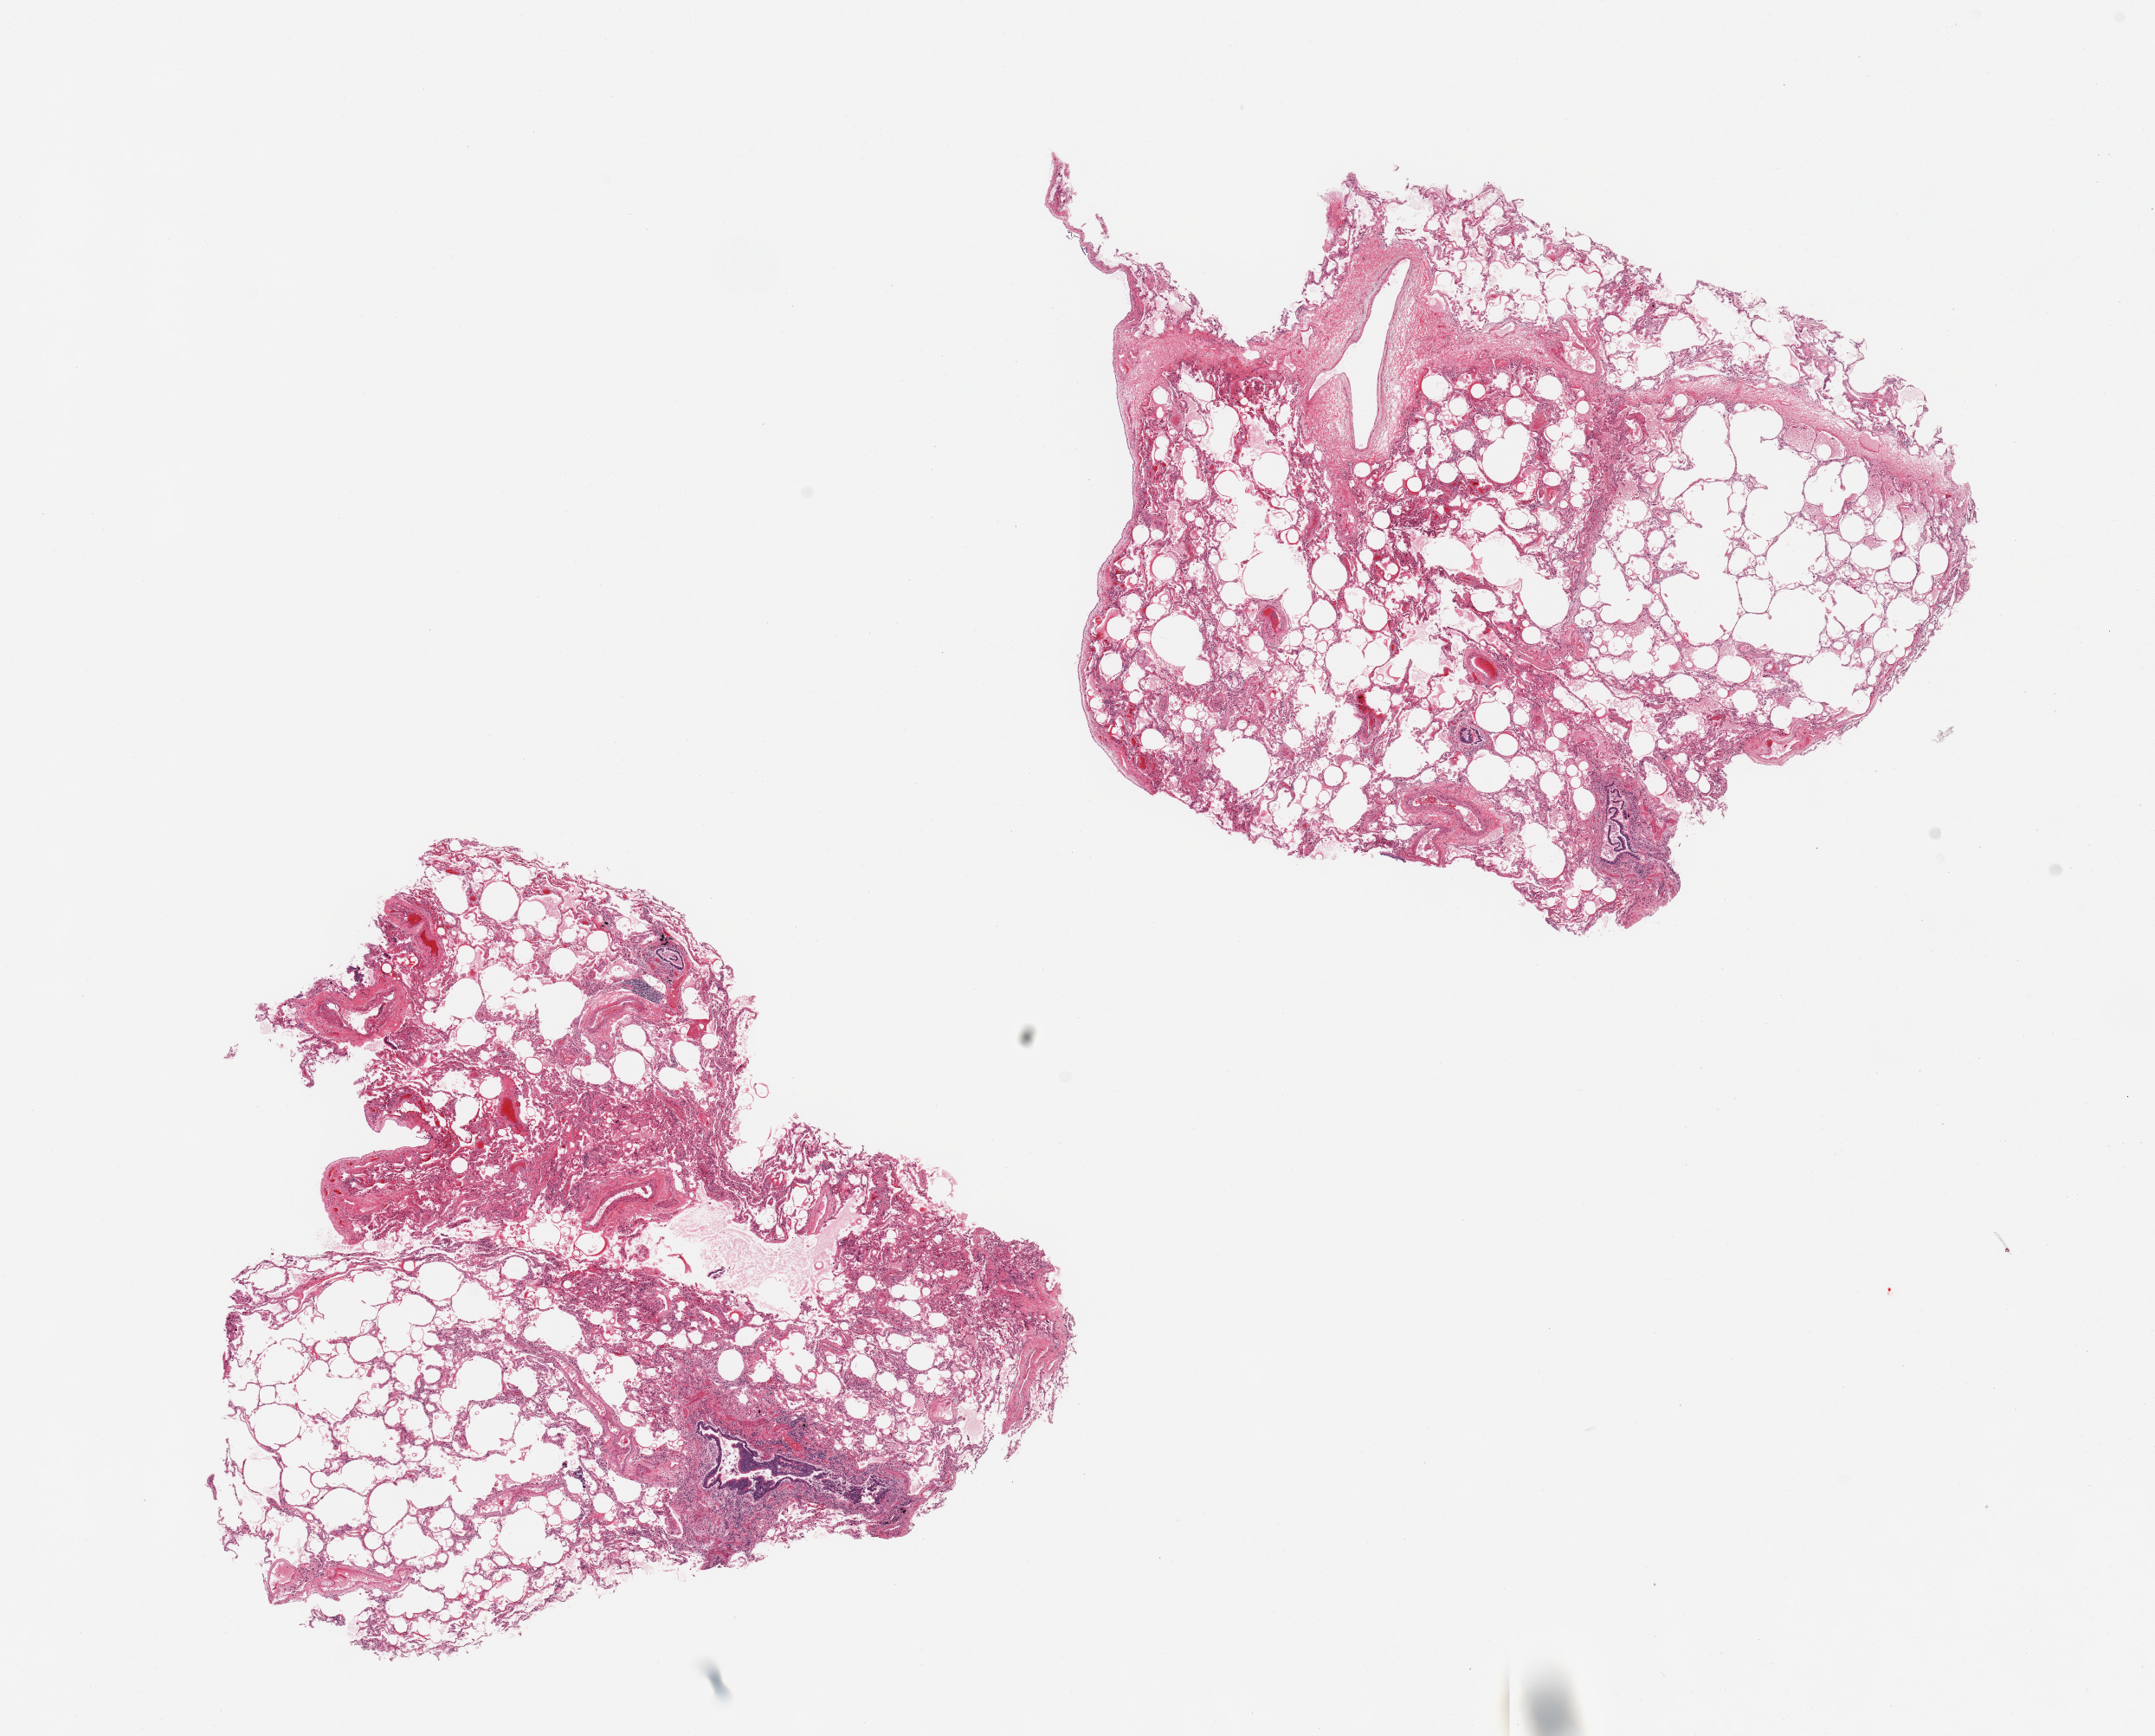
Whole-slide image, hematoxylin and eosin (H&E) stain, low-resolution overview of the scanned area, about 19.7 x 15.9 mm (from a 20x scan), PAXgene-fixed, paraffin-embedded tissue, section of lung (target tissue), tissue donor sample. Donor sex: male.
Pathologist's review note for this sample: 2 pieces. Emphysema and patchy fibrosis.